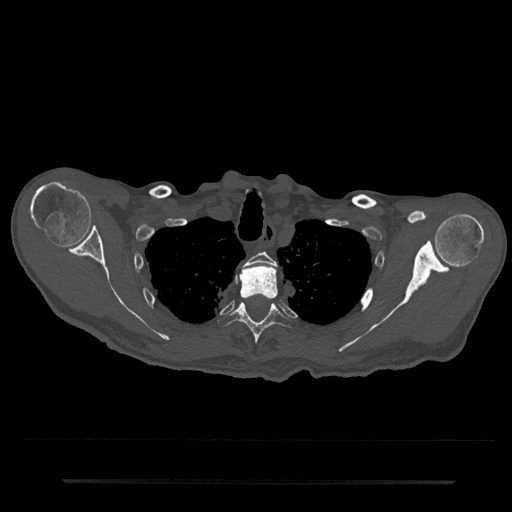
CT including the spine, one axial slice. Slice 643 of 797 in the series (ordered by position). Reconstruction kernel Br40s/3. Bone window (W 1800 / L 400 HU). 0.5 mm slice thickness. 512 × 512 image matrix. Male patient, age 74 years. From the clinical record (not read from this slice): primary cancer: prostate.
Outlined on this slice (semi-automatic segmentation, software-assisted and operator-edited):
- T2 vertebra: bounding box (x1, y1, x2, y2) in pixels: (243, 252, 277, 267)
- T3 vertebra: (240, 265, 279, 299)
- T4 vertebra: (218, 302, 298, 344)